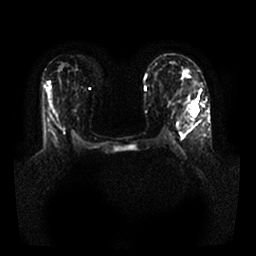
Breast MRI, one axial slice. Position 18 of 25 along the scan axis. Diffusion-weighted series; image 2 of 4 stored at this slice position (different b-values; order by instance number). 1.5 T. 4 mm slice thickness. 256 × 256 image matrix. Female patient.
Annotated regions visible in this slice (manually delineated by an expert):
- tumour on diffusion-weighted imaging: bounding box <191,101,197,115> (left, top, right, bottom; pixels)